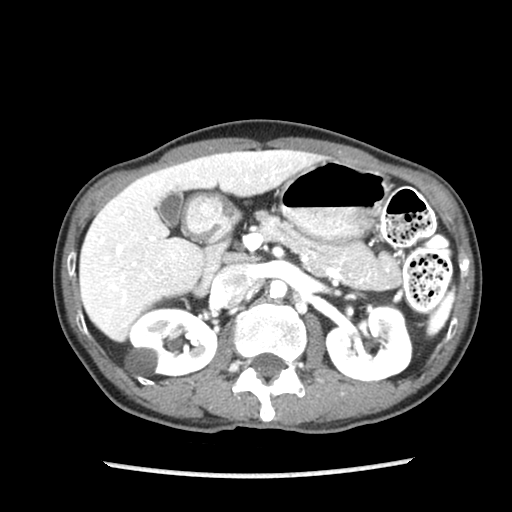
Contrast-enhanced abdominal CT (liver protocol), one axial slice. Slice 47 of 87 in the series (ordered by position). Reconstruction kernel STANDARD. 140 kVp. Soft-tissue window (W 400 / L 40 HU). 2.5 mm slice thickness. 512 × 512 image matrix. Case-level facts recorded for this patient, not image findings: diagnosis: hepatocellular carcinoma (patient treated with transarterial chemoembolisation; whether this scan precedes or follows treatment is not stated here); TNM stage (as recorded): Stage-IIIB; Child-Pugh class: A.
Structures marked on this image (semi-automatic segmentation, software-assisted and operator-edited):
- liver parenchyma outside the tumour (the mass and vessels are separate outlines, so this box may not span the whole liver): bounding box (x1, y1, x2, y2) in pixels: (80, 150, 326, 340)
- liver vessels: (91, 153, 275, 304)